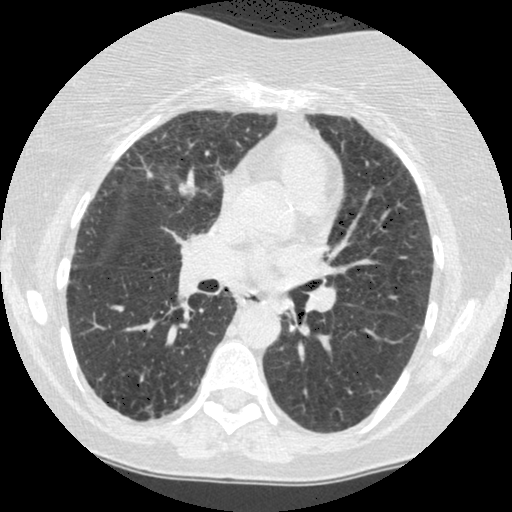
Low-dose screening chest CT, axial slice. Baseline annual screen. Lung window (W 1500 / L -600 HU). 1.25 mm slice thickness. Standard (soft-tissue) reconstruction kernel (STANDARD). 120 kVp. 512 × 512 image matrix. Female participant, aged 60 years at enrolment. Former smoker at enrolment.
Expert reader's lesion annotation, box from (x=267, y=291) to (x=308, y=332) px. The screening reader recorded 2 non-calcified nodules or masses ≥4 mm on this exam (right lower lobe, left lower lobe); which of them this box marks is not recorded. Official screen result: positive, change unspecified: nodule(s) >= 4 mm or enlarging nodule(s), mass(es), or other non-specific abnormalities suspicious for lung cancer. Later outcome: lung cancer diagnosed 794 days after this screen (after the third annual screen) — small cell carcinoma, NOS, left lower lobe, undifferentiated (G4), stage IV (AJCC 6th edition), 69 mm at pathology.